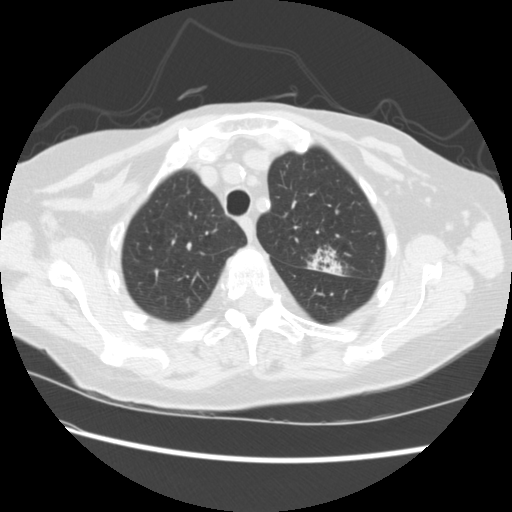
Low-dose screening chest CT, one axial slice. Slice 177 of 224 in the series (ordered by position). 120 kVp. Lung window (W 1500 / L -600 HU). 512 × 512 image matrix, field of view 340 × 340 mm.
Annotated regions visible in this slice (expert manual segmentation):
- lesion 1 (tumor, upper lobe of left lung): bounding box <307,249,343,276> (left, top, right, bottom; pixels)